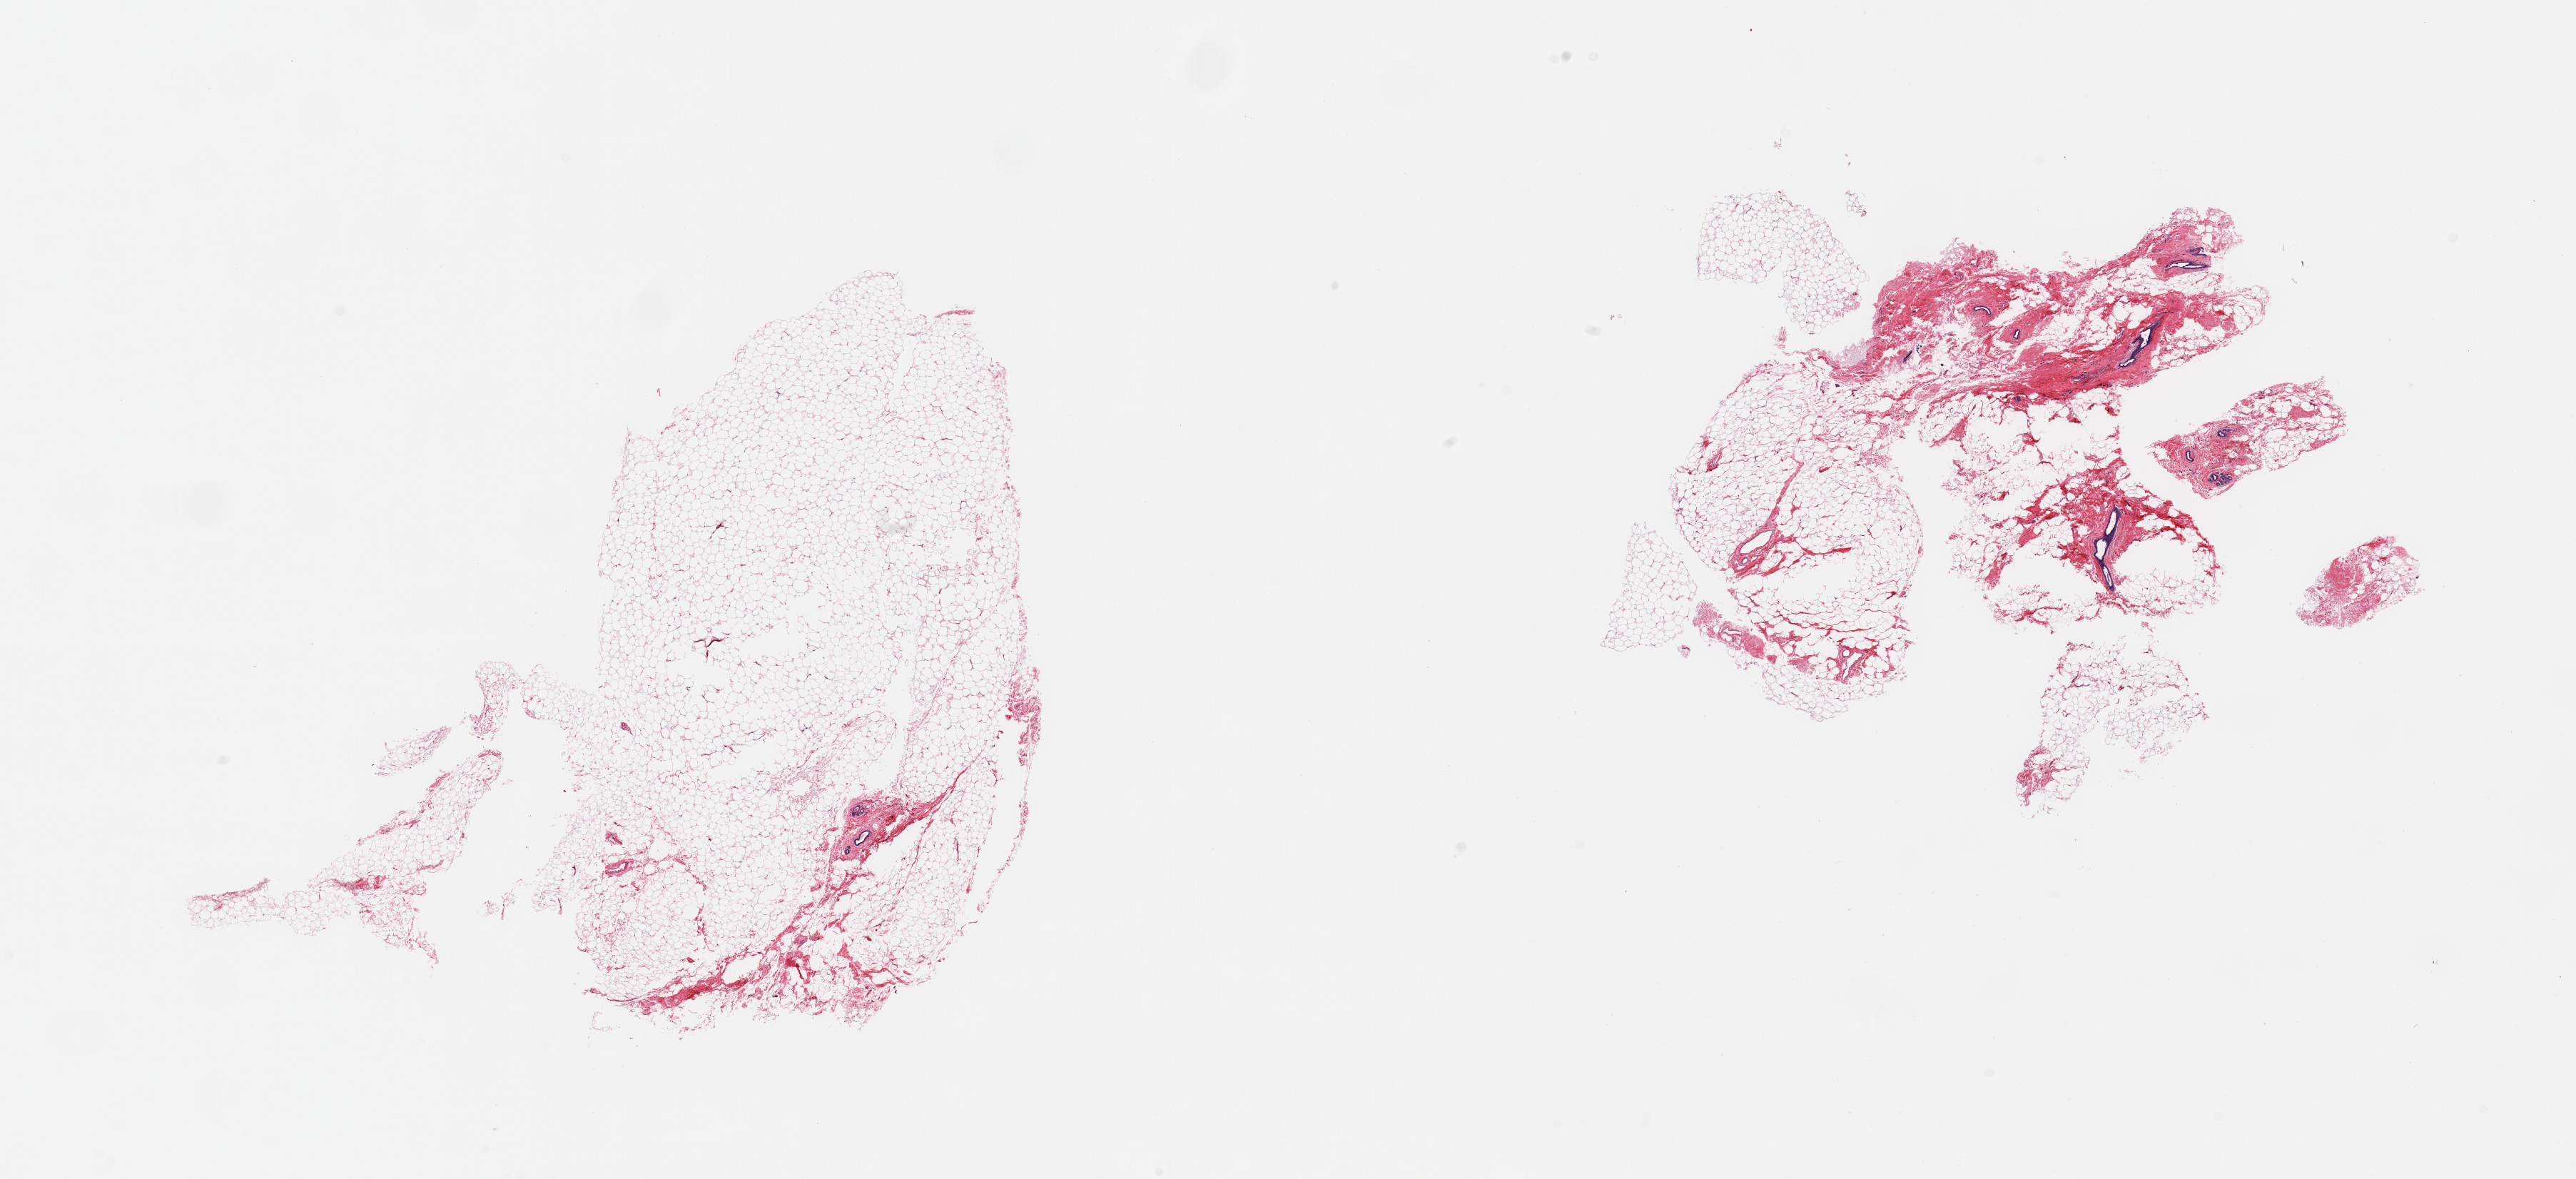
Whole-slide image, H&E stain, low-resolution overview of the scanned area, about 28.5 x 13.1 mm. PAXgene-fixed paraffin-embedded (PFPE) section. Section of breast (target tissue). Donor tissue sample. Female donor.
Review note (as recorded): 2 pieces; mostly fat with <10 and 25% fibrocollagenous tissue with scattered duct and lobules.